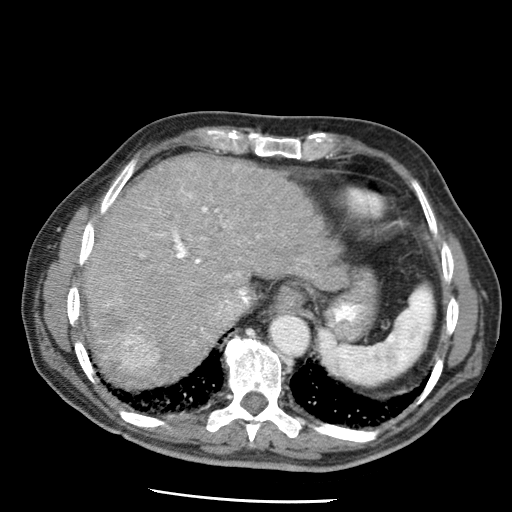
Contrast-enhanced abdominal CT (liver protocol), one axial slice; slice 53 of 79 in the series (ordered by position); reconstruction kernel STANDARD; 120 kVp; soft-tissue window (W 400 / L 40 HU); 512 × 512 image matrix. Case-level facts recorded for this patient, not image findings: diagnosis: hepatocellular carcinoma (patient treated with transarterial chemoembolisation; whether this scan precedes or follows treatment is not stated here); TNM stage (as recorded): Stage-IIIA; Child-Pugh class: A; tumour differentiation: moderately differentiated; tumour size: 7 cm.
Structures marked on this image (semi-automatically segmented with operator editing):
- abdominal aorta: bounding box <272,317,308,356> (left, top, right, bottom; pixels)
- liver parenchyma outside the tumour (the mass and vessels are separate outlines, so this box may not span the whole liver): <82,156,336,382>
- mass: <113,329,159,375>
- liver vessels: <106,188,259,342>